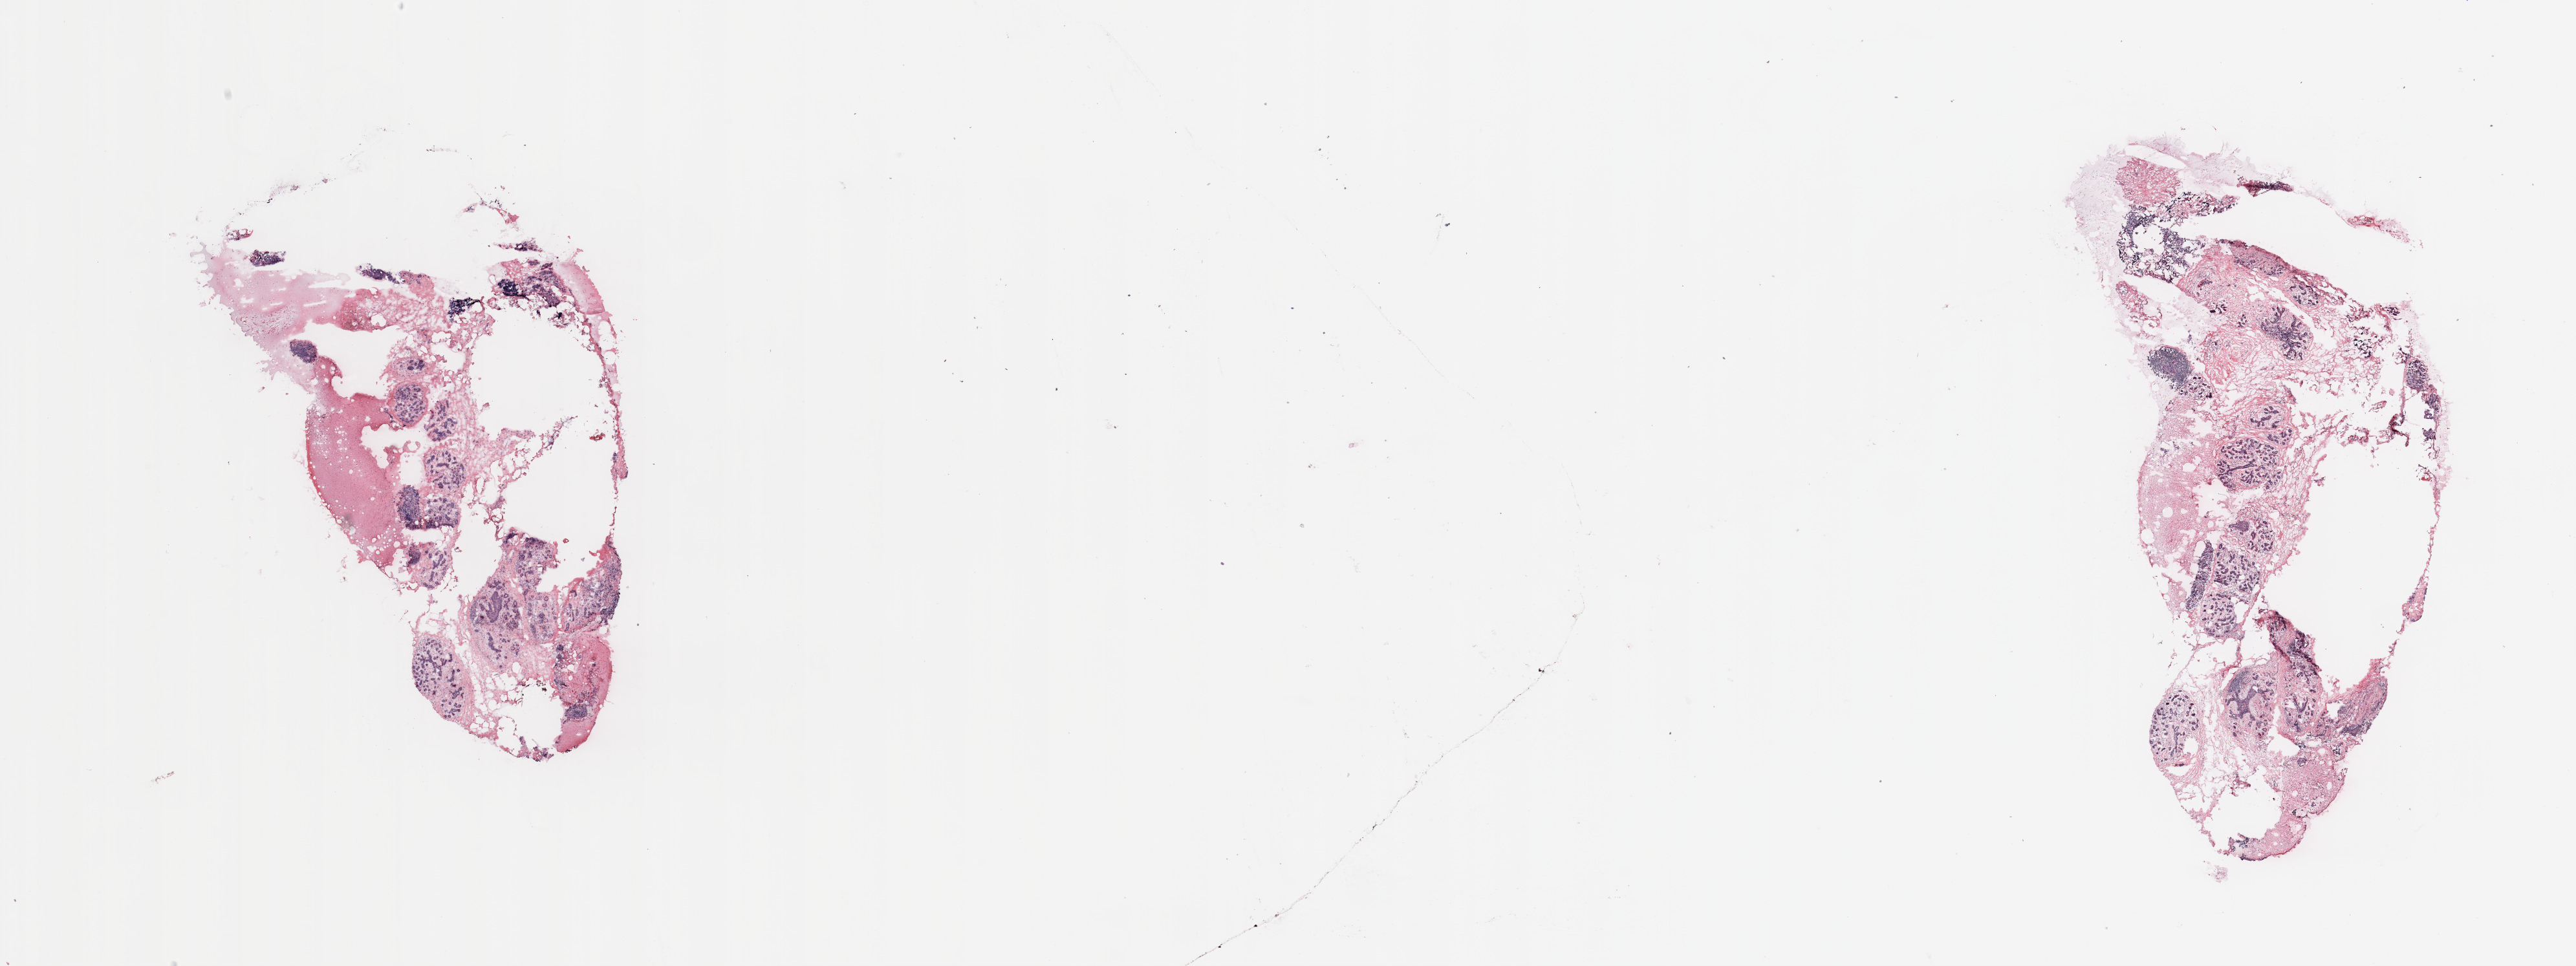
Digitized H&E tissue section (whole slide) — low-resolution overview of the scanned area, about 31.5 x 11.8 mm (from a 20x scan). Female, 48 y/o.
Specimen: tumour tissue sample, breast.